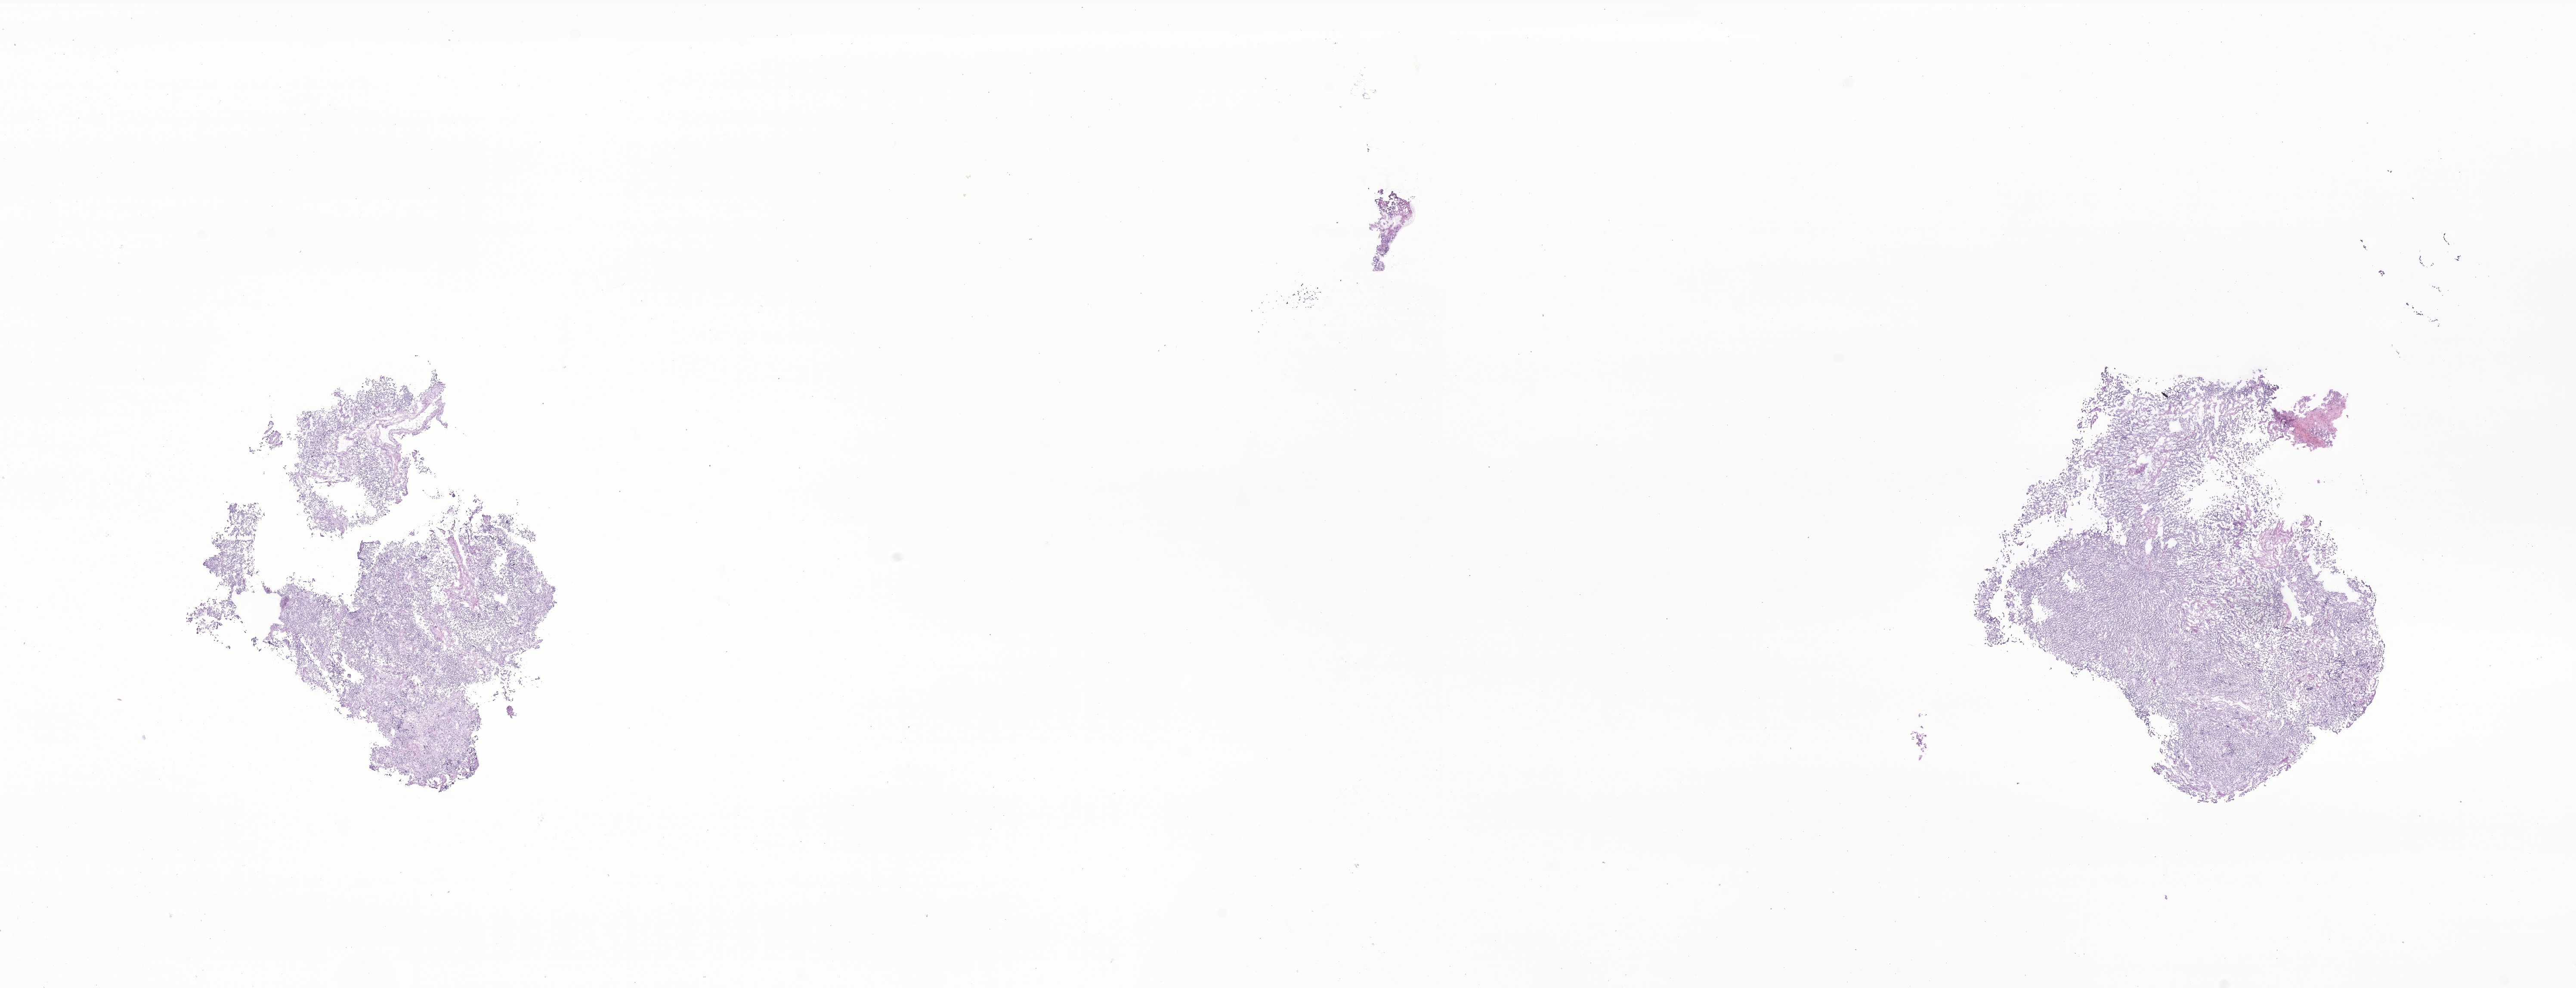
Whole-slide image, hematoxylin and eosin (H&E) stain of tumor tissue from the brain stem, low-resolution overview of the scanned area, about 25.2 x 9.7 mm; frozen section (OCT-embedded). Patient: male, age 968 days (about 2.7 years).
Diagnosis (ICD-O-3 morphology term): Medulloblastoma, NOS.